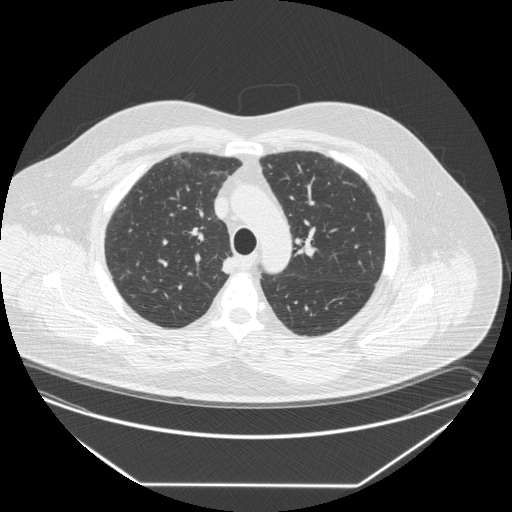
Low-dose screening chest CT, one axial slice. Position 200 of 258 along the scan axis. Lung window (W 1500 / L -600 HU). 2.5 mm slice thickness. 512 × 512 image matrix, field of view 440 × 440 mm.
Annotated regions visible in this slice (manually delineated by an expert):
- lesion 1 (tumor, upper lobe of right lung): bounding box [x1, y1, x2, y2] px = [222, 256, 237, 274]